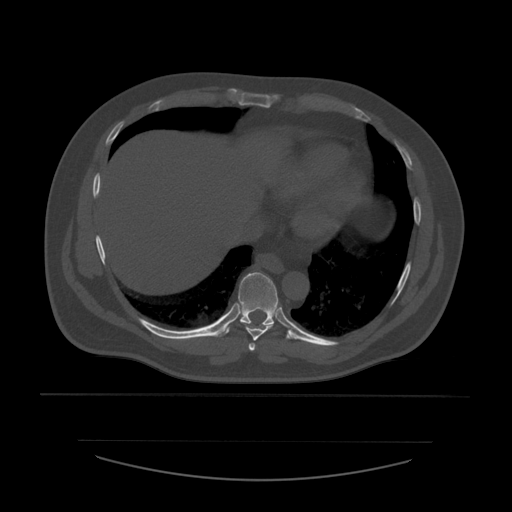
CT including the spine, one axial slice; position 327 of 532 along the scan axis; 120 kVp; bone window (W 1800 / L 400 HU); 1.25 mm slice thickness; 512 × 512 image matrix, field of view 441 × 441 mm. Patient age 44 years. From the clinical record (not read from this slice): primary cancer: soft tissue sarcoma.
Structures marked on this image (semi-automatic segmentation, software-assisted and operator-edited):
- T7 vertebra: bounding box (x1, y1, x2, y2) in pixels: (249, 343, 256, 353)
- T8 vertebra: (242, 323, 274, 341)
- T9 vertebra: (217, 272, 293, 339)